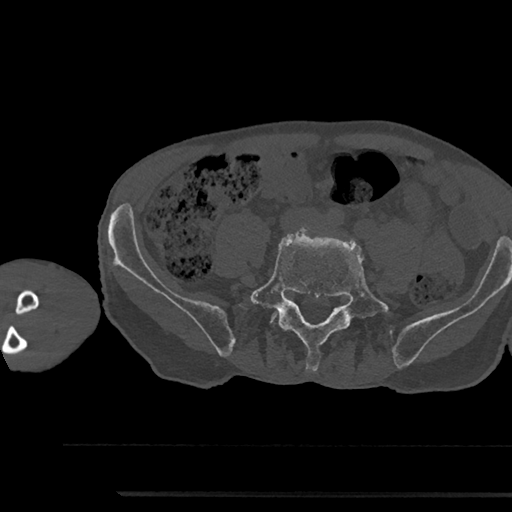
CT including the spine, one axial slice. Position 350 of 797 along the scan axis. 120 kVp. Bone window (W 1800 / L 400 HU). 0.5 mm slice thickness. 512 × 512 image matrix. Patient: male, 79 years. Case-level facts recorded for this patient, not image findings: primary cancer: prostate.
Annotated regions visible in this slice (semi-automatic segmentation, software-assisted and operator-edited):
- L5 vertebra: box from (x=243, y=229) to (x=393, y=370) px